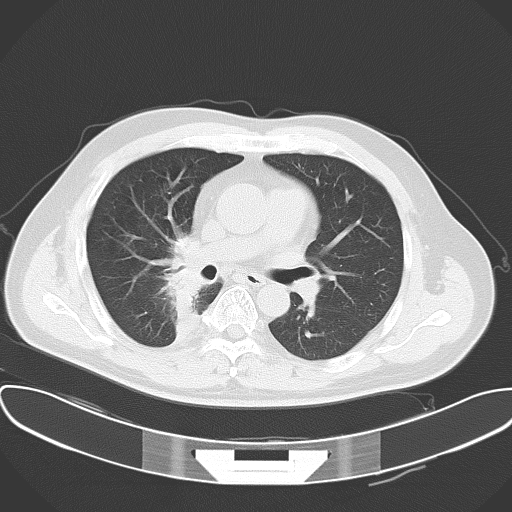
Chest CT, one axial slice; slice 32 of 57 in the series (ordered by position); 120 kVp; lung window (W 1500 / L -600 HU); 5 mm slice thickness; 512 × 512 image matrix, field of view 388 × 388 mm. Male patient, age 48 years. From the clinical record (not read from this slice): clinical TNM (as recorded): T1a N1 M1c.
Annotated regions visible in this slice (bounding box drawn by a radiologist):
- lung tumour (recorded histology: adenocarcinoma): bounding box [x1, y1, x2, y2] px = [151, 231, 209, 306]